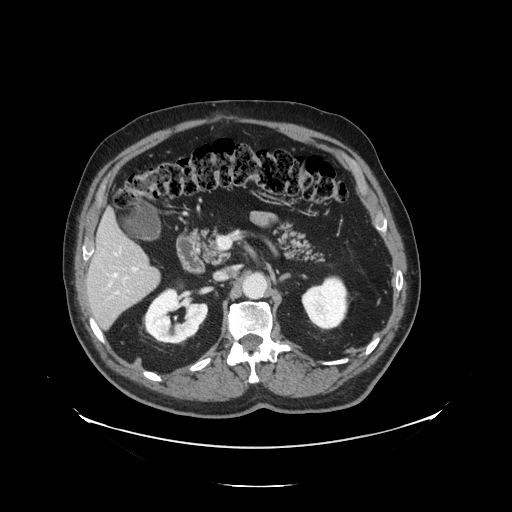
Contrast-enhanced abdominal CT, one axial slice; slice 68 of 138 in the series (ordered by position); reconstruction kernel STANDARD; intravenous contrast given; soft-tissue window (W 400 / L 40 HU); 512 × 512 image matrix, field of view 497 × 497 mm. Male patient, age 77 years. Case-level facts recorded for this patient, not image findings: diagnosis: colorectal cancer liver metastases, imaged before liver resection; multiple liver metastases: no; largest metastasis: 1.5 cm.
Annotated regions visible in this slice (manually delineated by an expert):
- hepatic veins: box from (x=113, y=274) to (x=116, y=278) px
- liver: (x=89, y=214)–(x=160, y=329)
- planned liver remnant (the part of the liver to remain after resection): (x=89, y=214)–(x=151, y=286)
- portal vein (with intrahepatic branches): (x=116, y=267)–(x=138, y=294)